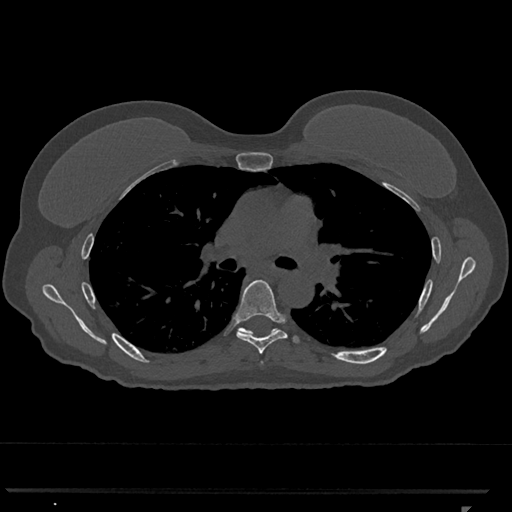
CT including the spine, one axial slice. Position 755 of 793 along the scan axis. 120 kVp. Bone window (W 1800 / L 400 HU). 512 × 512 image matrix. Patient: female, 62 years. Case-level facts recorded for this patient, not image findings: primary cancer: renal.
Annotated regions visible in this slice (semi-automatically segmented with operator editing):
- T6 vertebra: bounding box (x1, y1, x2, y2) in pixels: (235, 280, 287, 354)
- T7 vertebra: (238, 327, 276, 334)